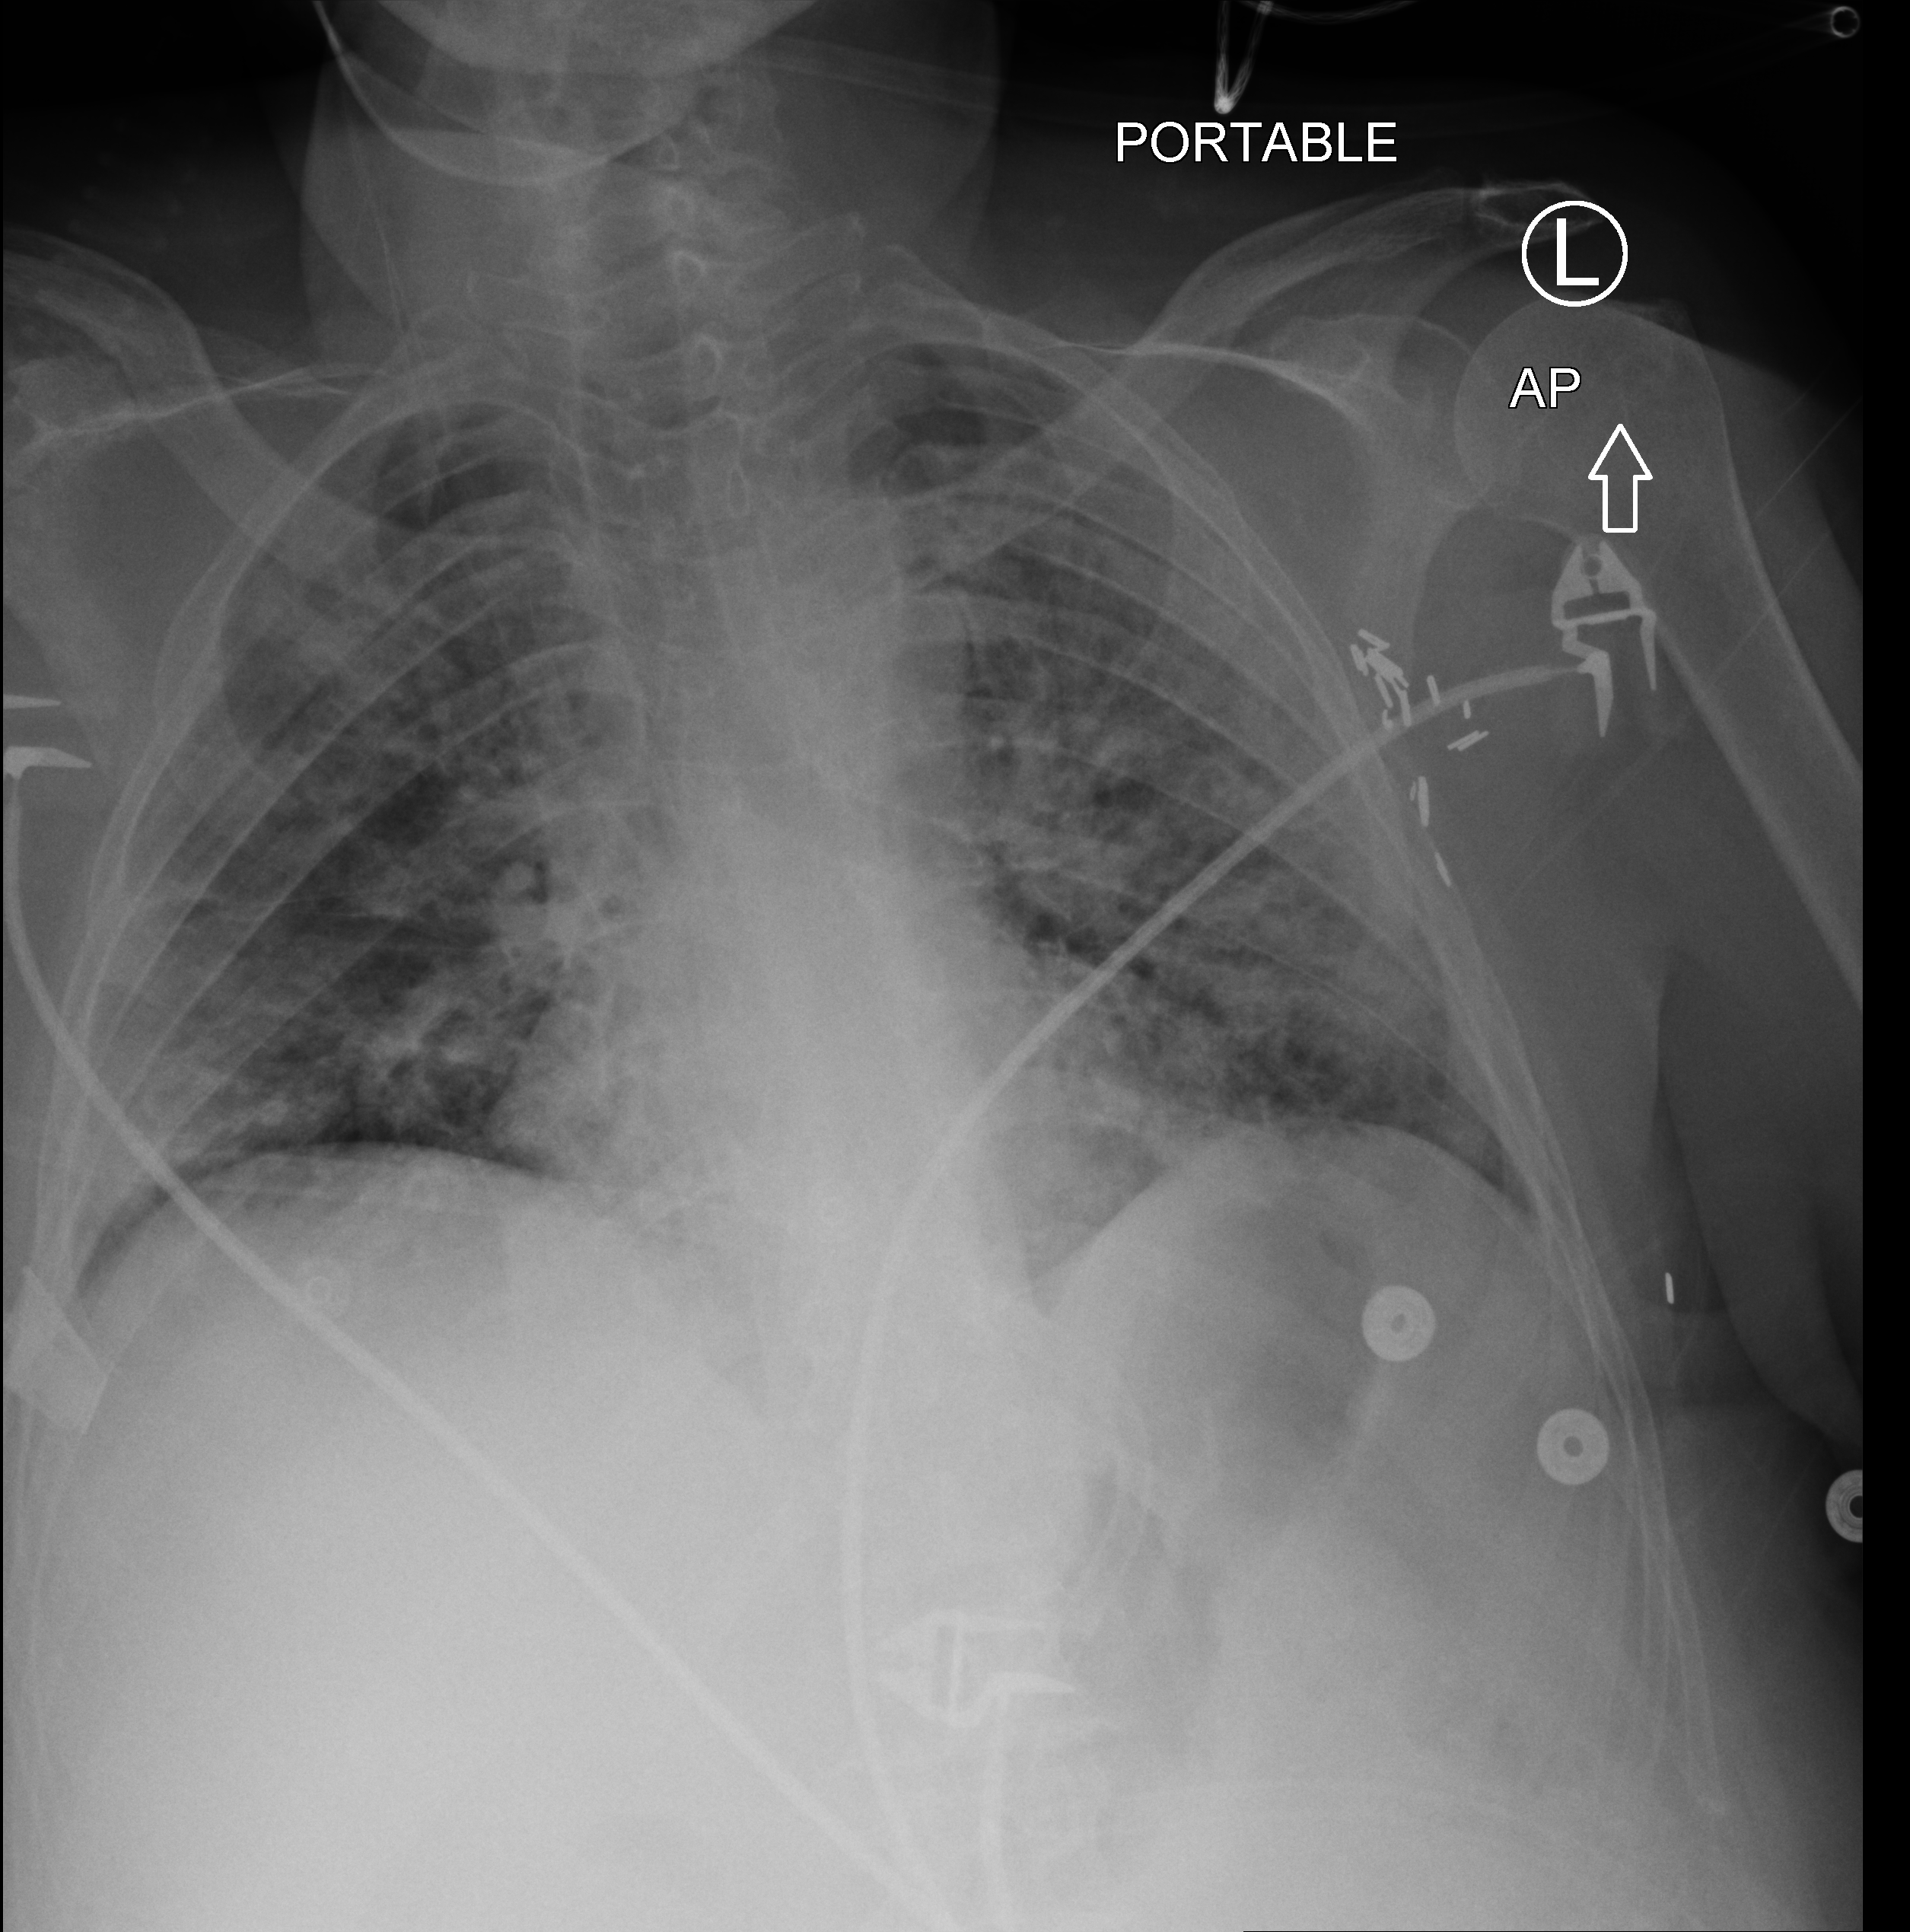
Bedside chest radiograph (computed radiography). Patient hospitalised with COVID-19; female, aged 60–74 years.
From the hospital-stay record, not from the radiograph (when in the stay this image was taken is not recorded): mechanically ventilated during this hospital stay: yes.